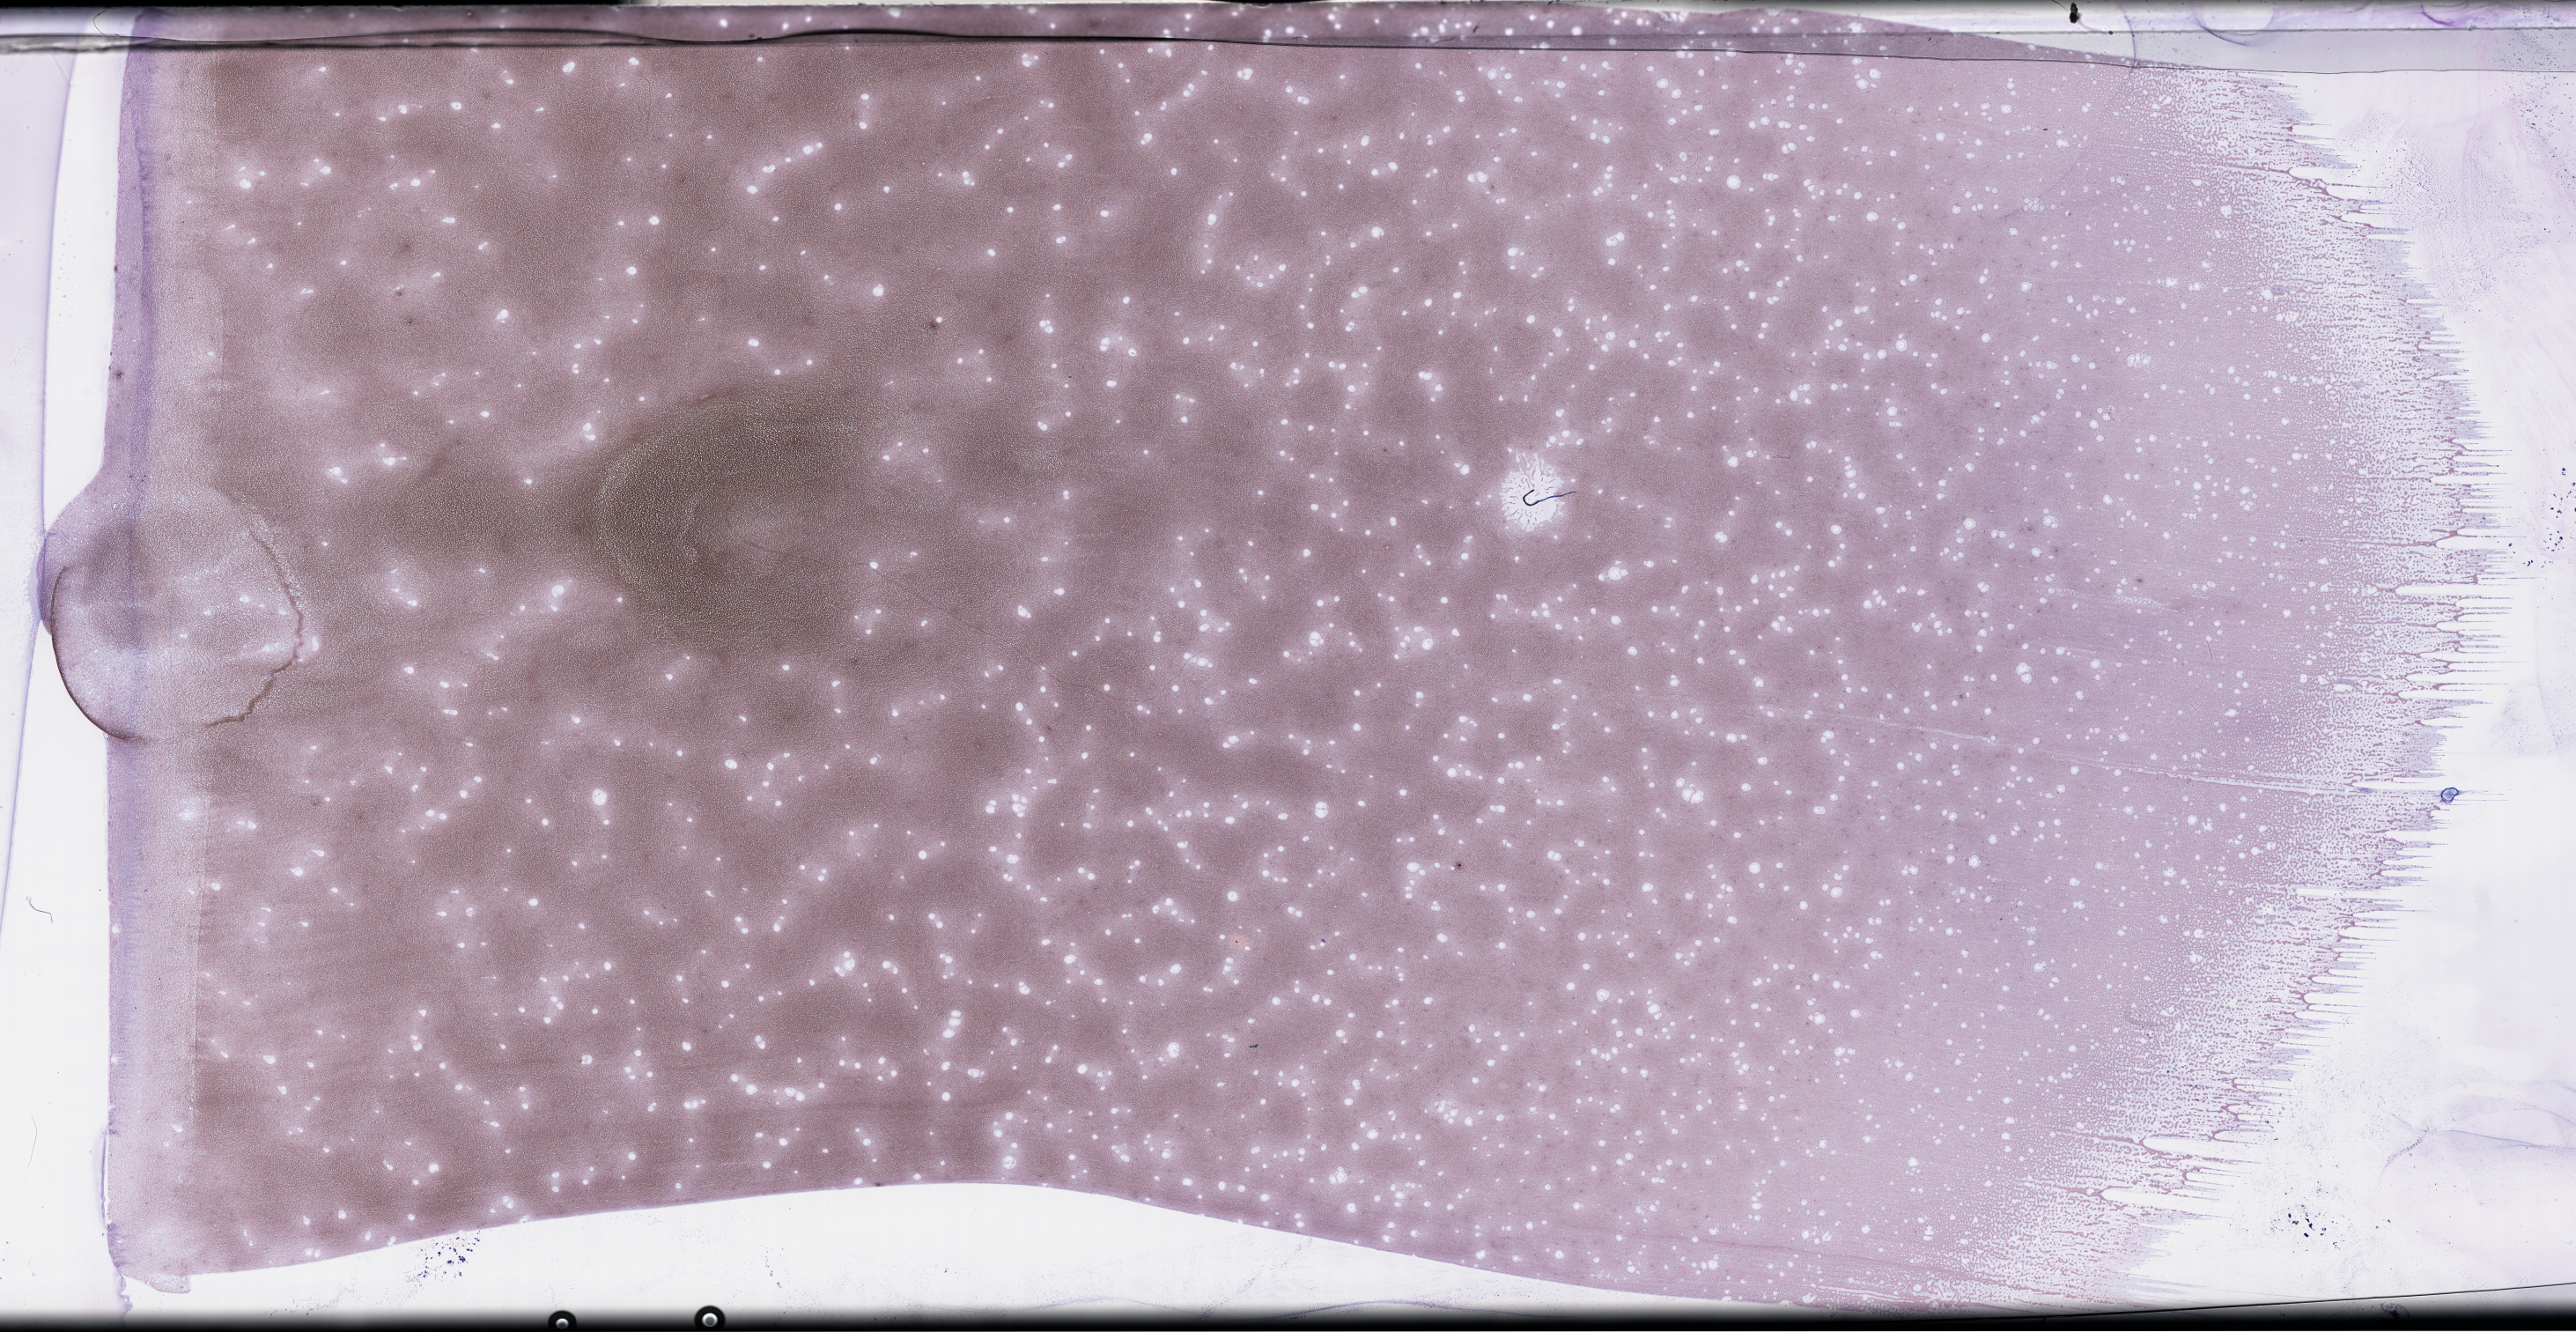
Wright-Giemsa-stained whole blood smear, whole-slide image, whole scanned area (about 47.2 x 24.4 mm) shown as a low-resolution overview, EDTA-anticoagulated smear. Patient: female.
From a patient with: Plasma Cell Myeloma.